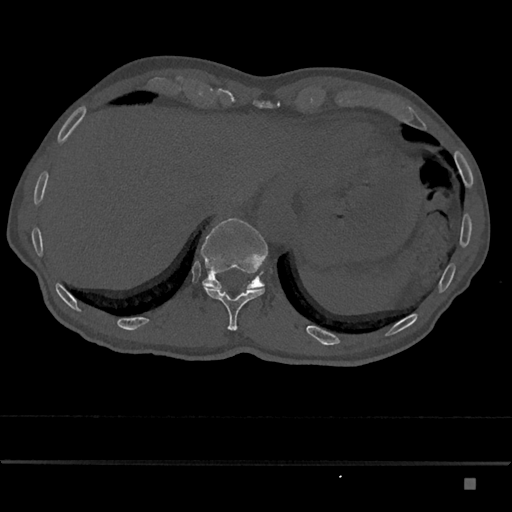
CT including the spine, one axial slice; position 652 of 797 along the scan axis; reconstruction kernel Br40s/3; bone window (W 1800 / L 400 HU); 0.5 mm slice thickness; 512 × 512 image matrix, field of view 390 × 390 mm. Male patient, age 72 years. From the clinical record (not read from this slice): primary cancer: prostate.
Structures marked on this image (semi-automatic segmentation, software-assisted and operator-edited):
- T11 vertebra: bounding box [x1, y1, x2, y2] px = [202, 283, 265, 331]
- T12 vertebra: [201, 218, 268, 289]